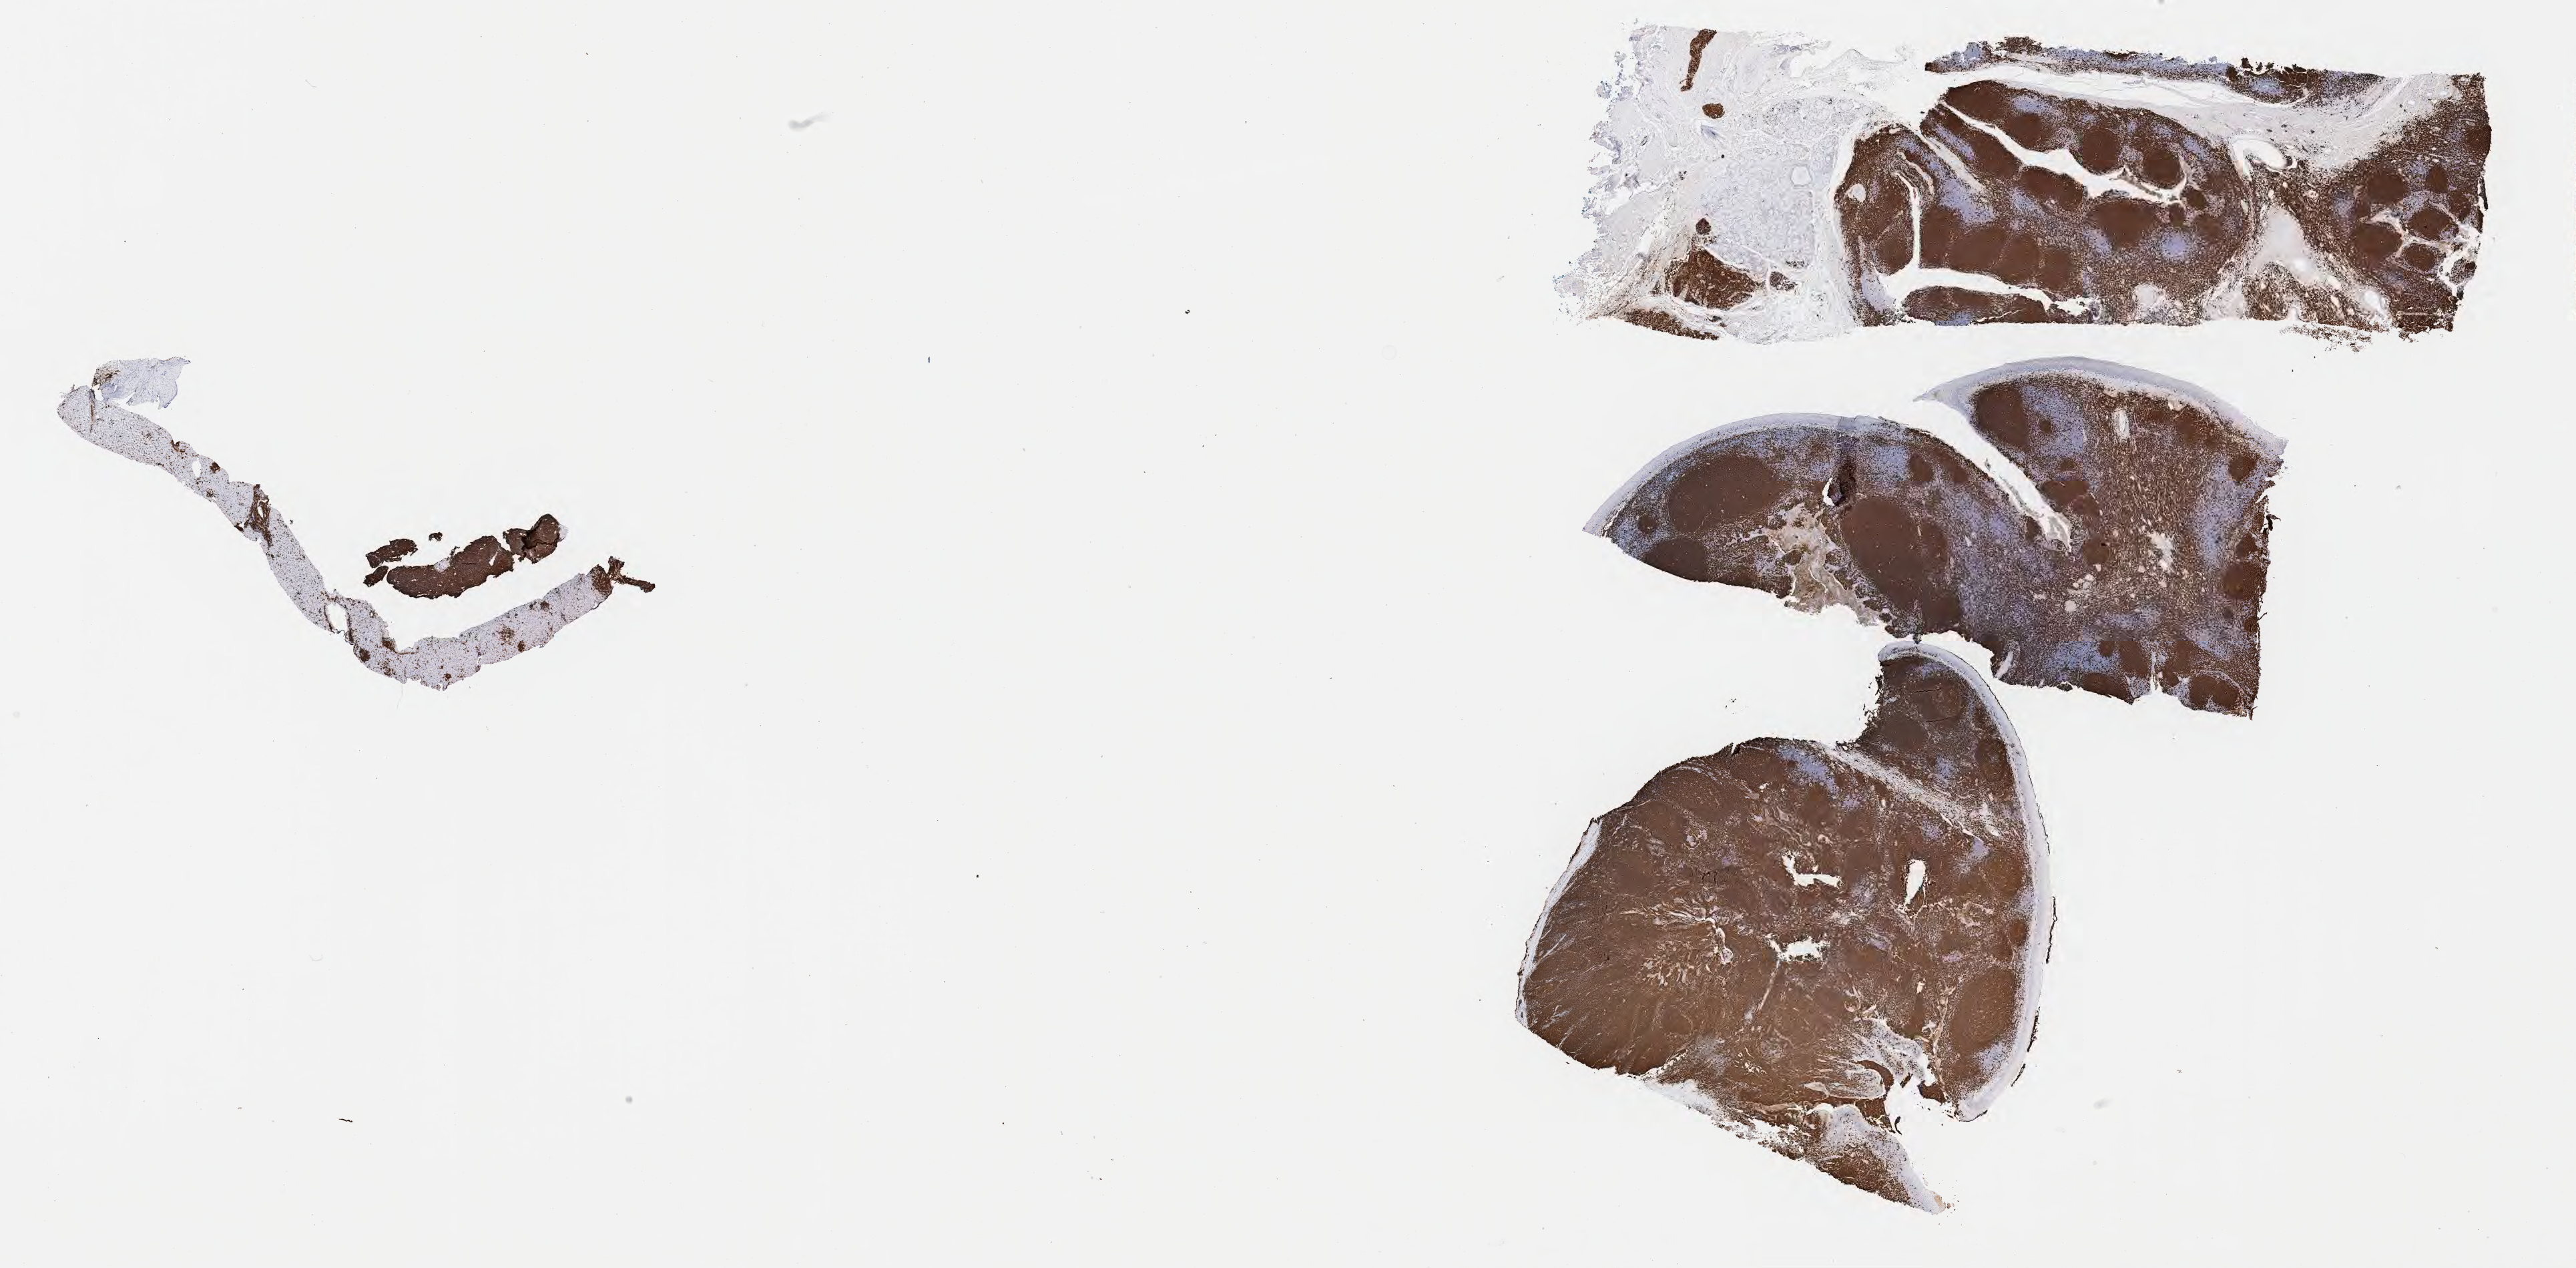
Whole-slide image, immunohistochemical stain for CD20, low-resolution overview of the scanned area, about 31.2 x 15.4 mm. Specimen: tumor tissue. Site: liver. Patient: male, age at initial diagnosis 7 years.
Diagnosis: Burkitt lymphoma, NOS.